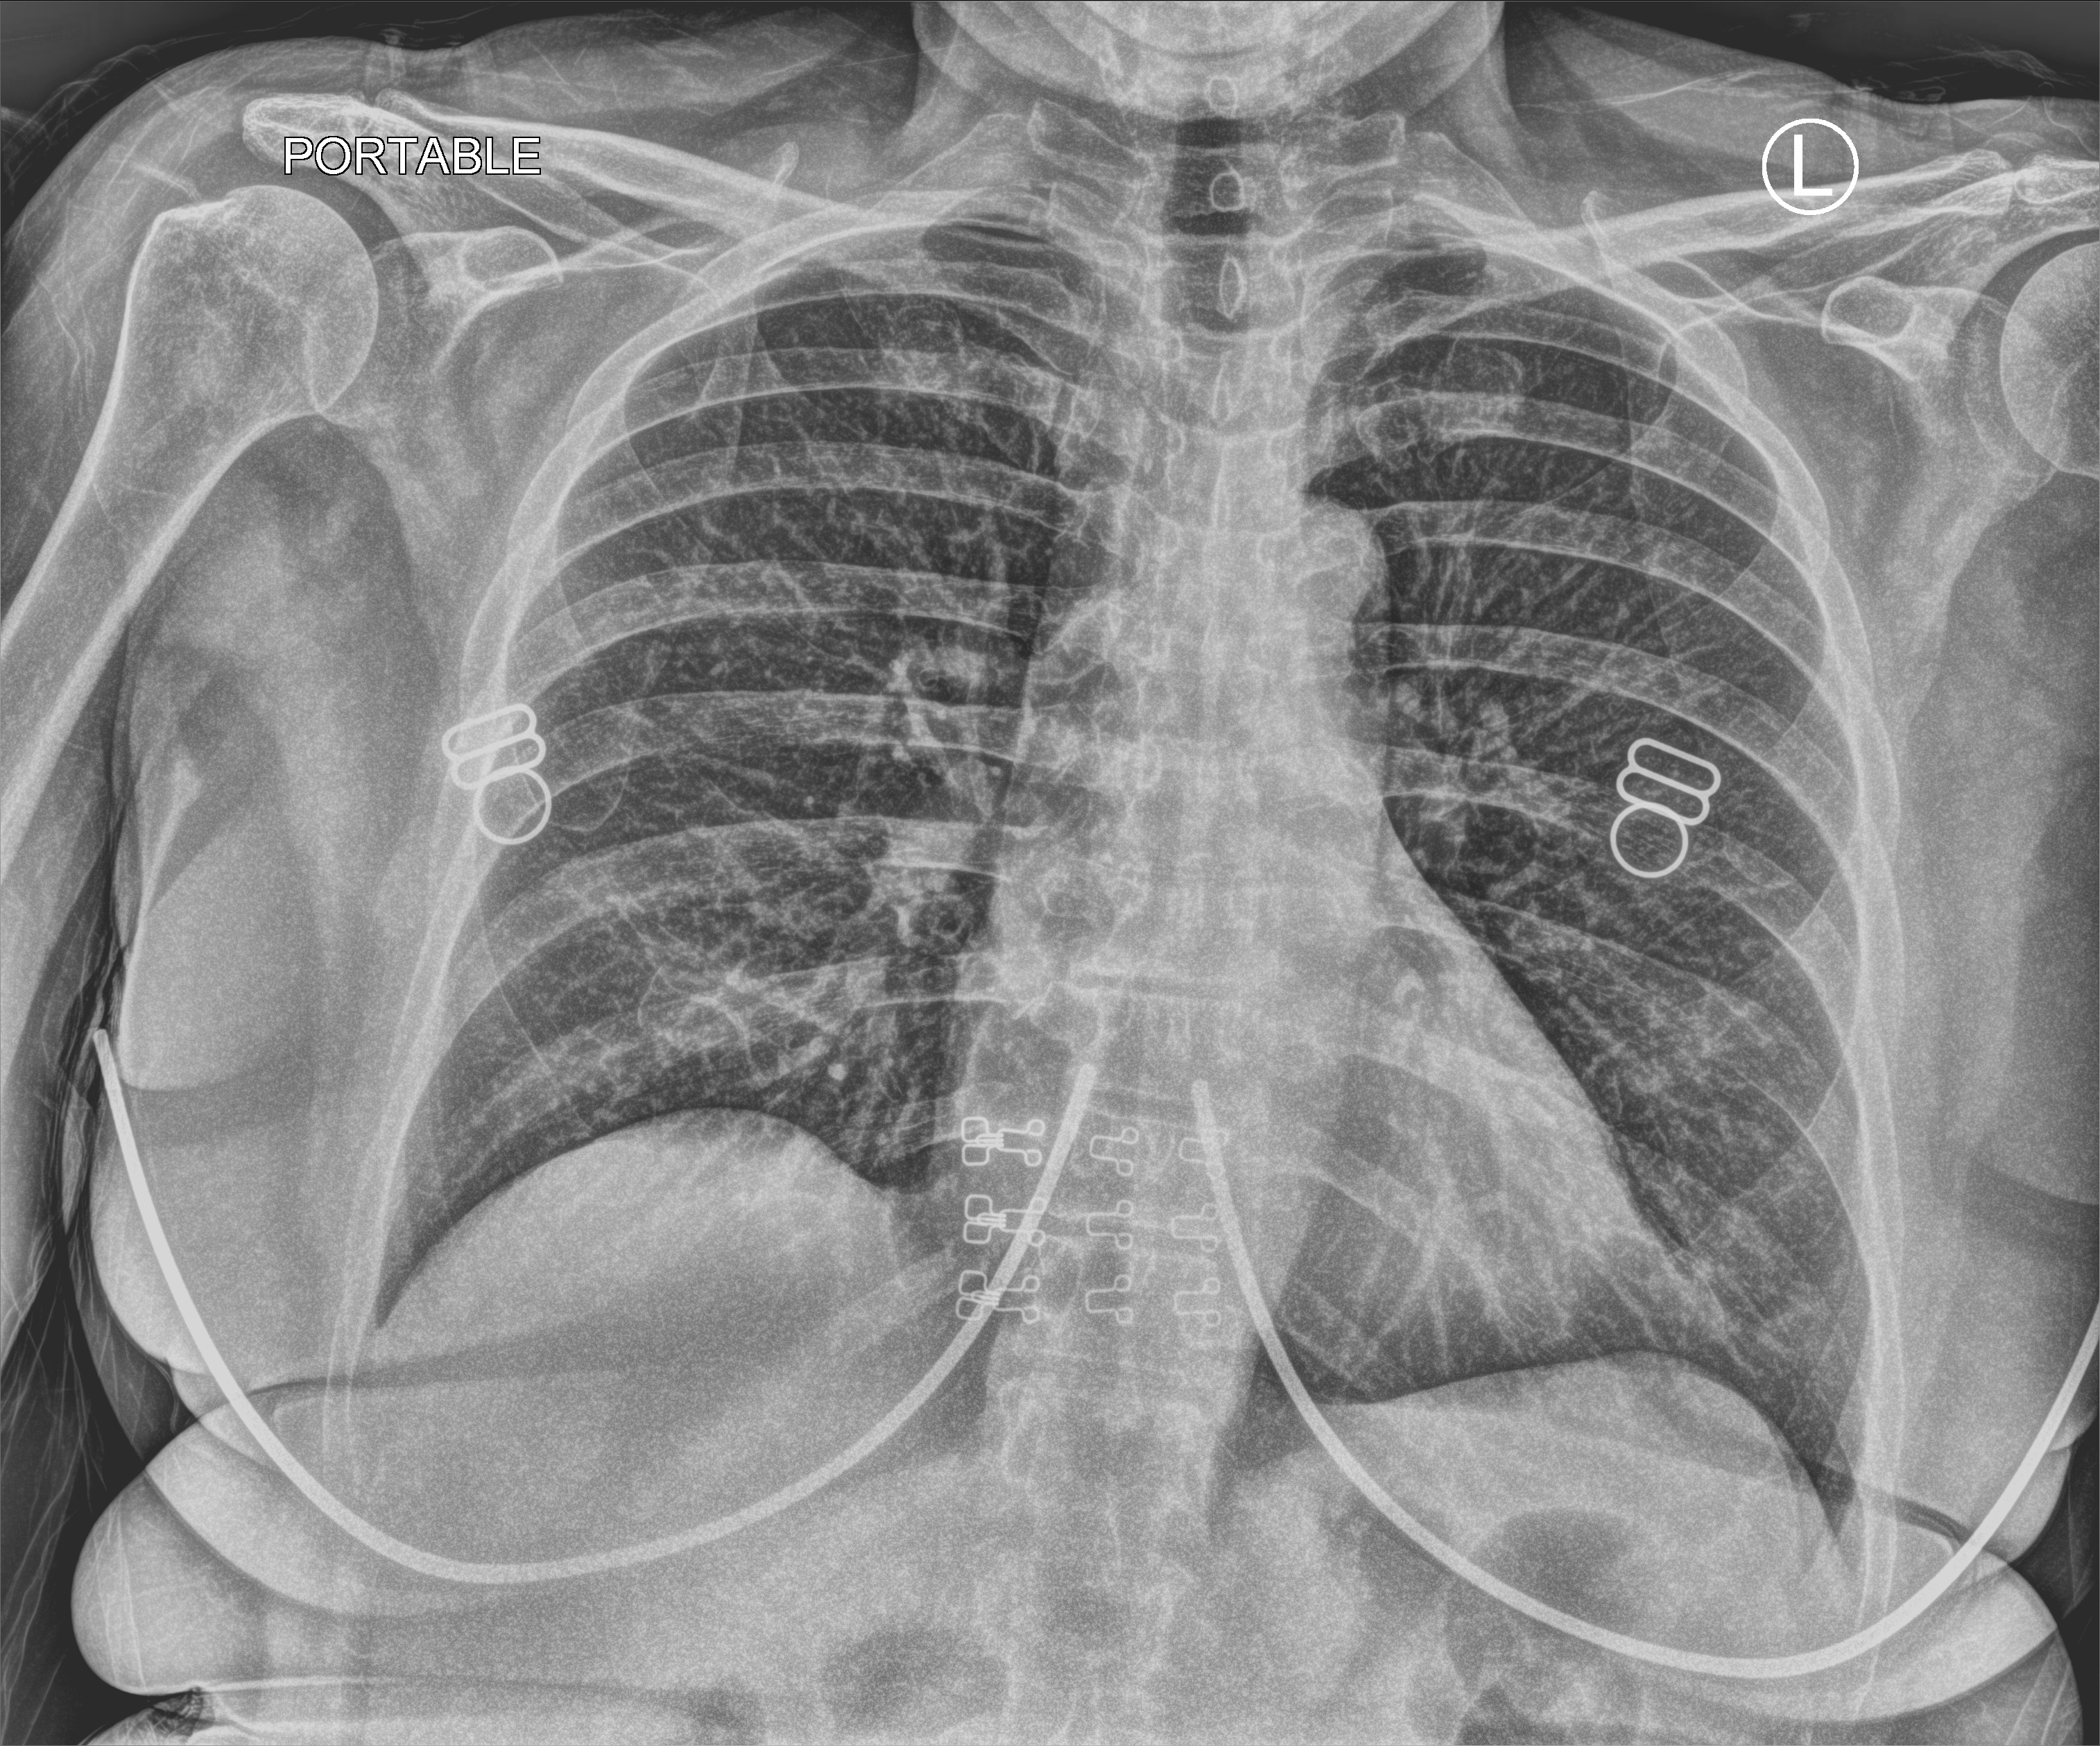
Chest X-ray (portable). Female patient hospitalised with COVID-19, age 18–59 years.
Admission-level facts for this patient (not findings on this image; timing relative to this image not recorded): admitted to intensive care during this hospital stay: no.